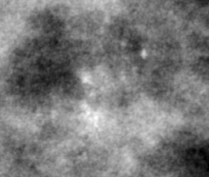
Cropped region of a digitized screen-film mammogram centred on a radiologist-marked abnormality; left breast; CC view; BI-RADS breast density category 3 (scale 1–4).
Finding: calcifications, morphology pleomorphic, distribution clustered; BI-RADS assessment category 4; subtlety rating 2 on a 1 (subtle) to 5 (obvious) scale; pathology result (as recorded, not read from the image): benign.